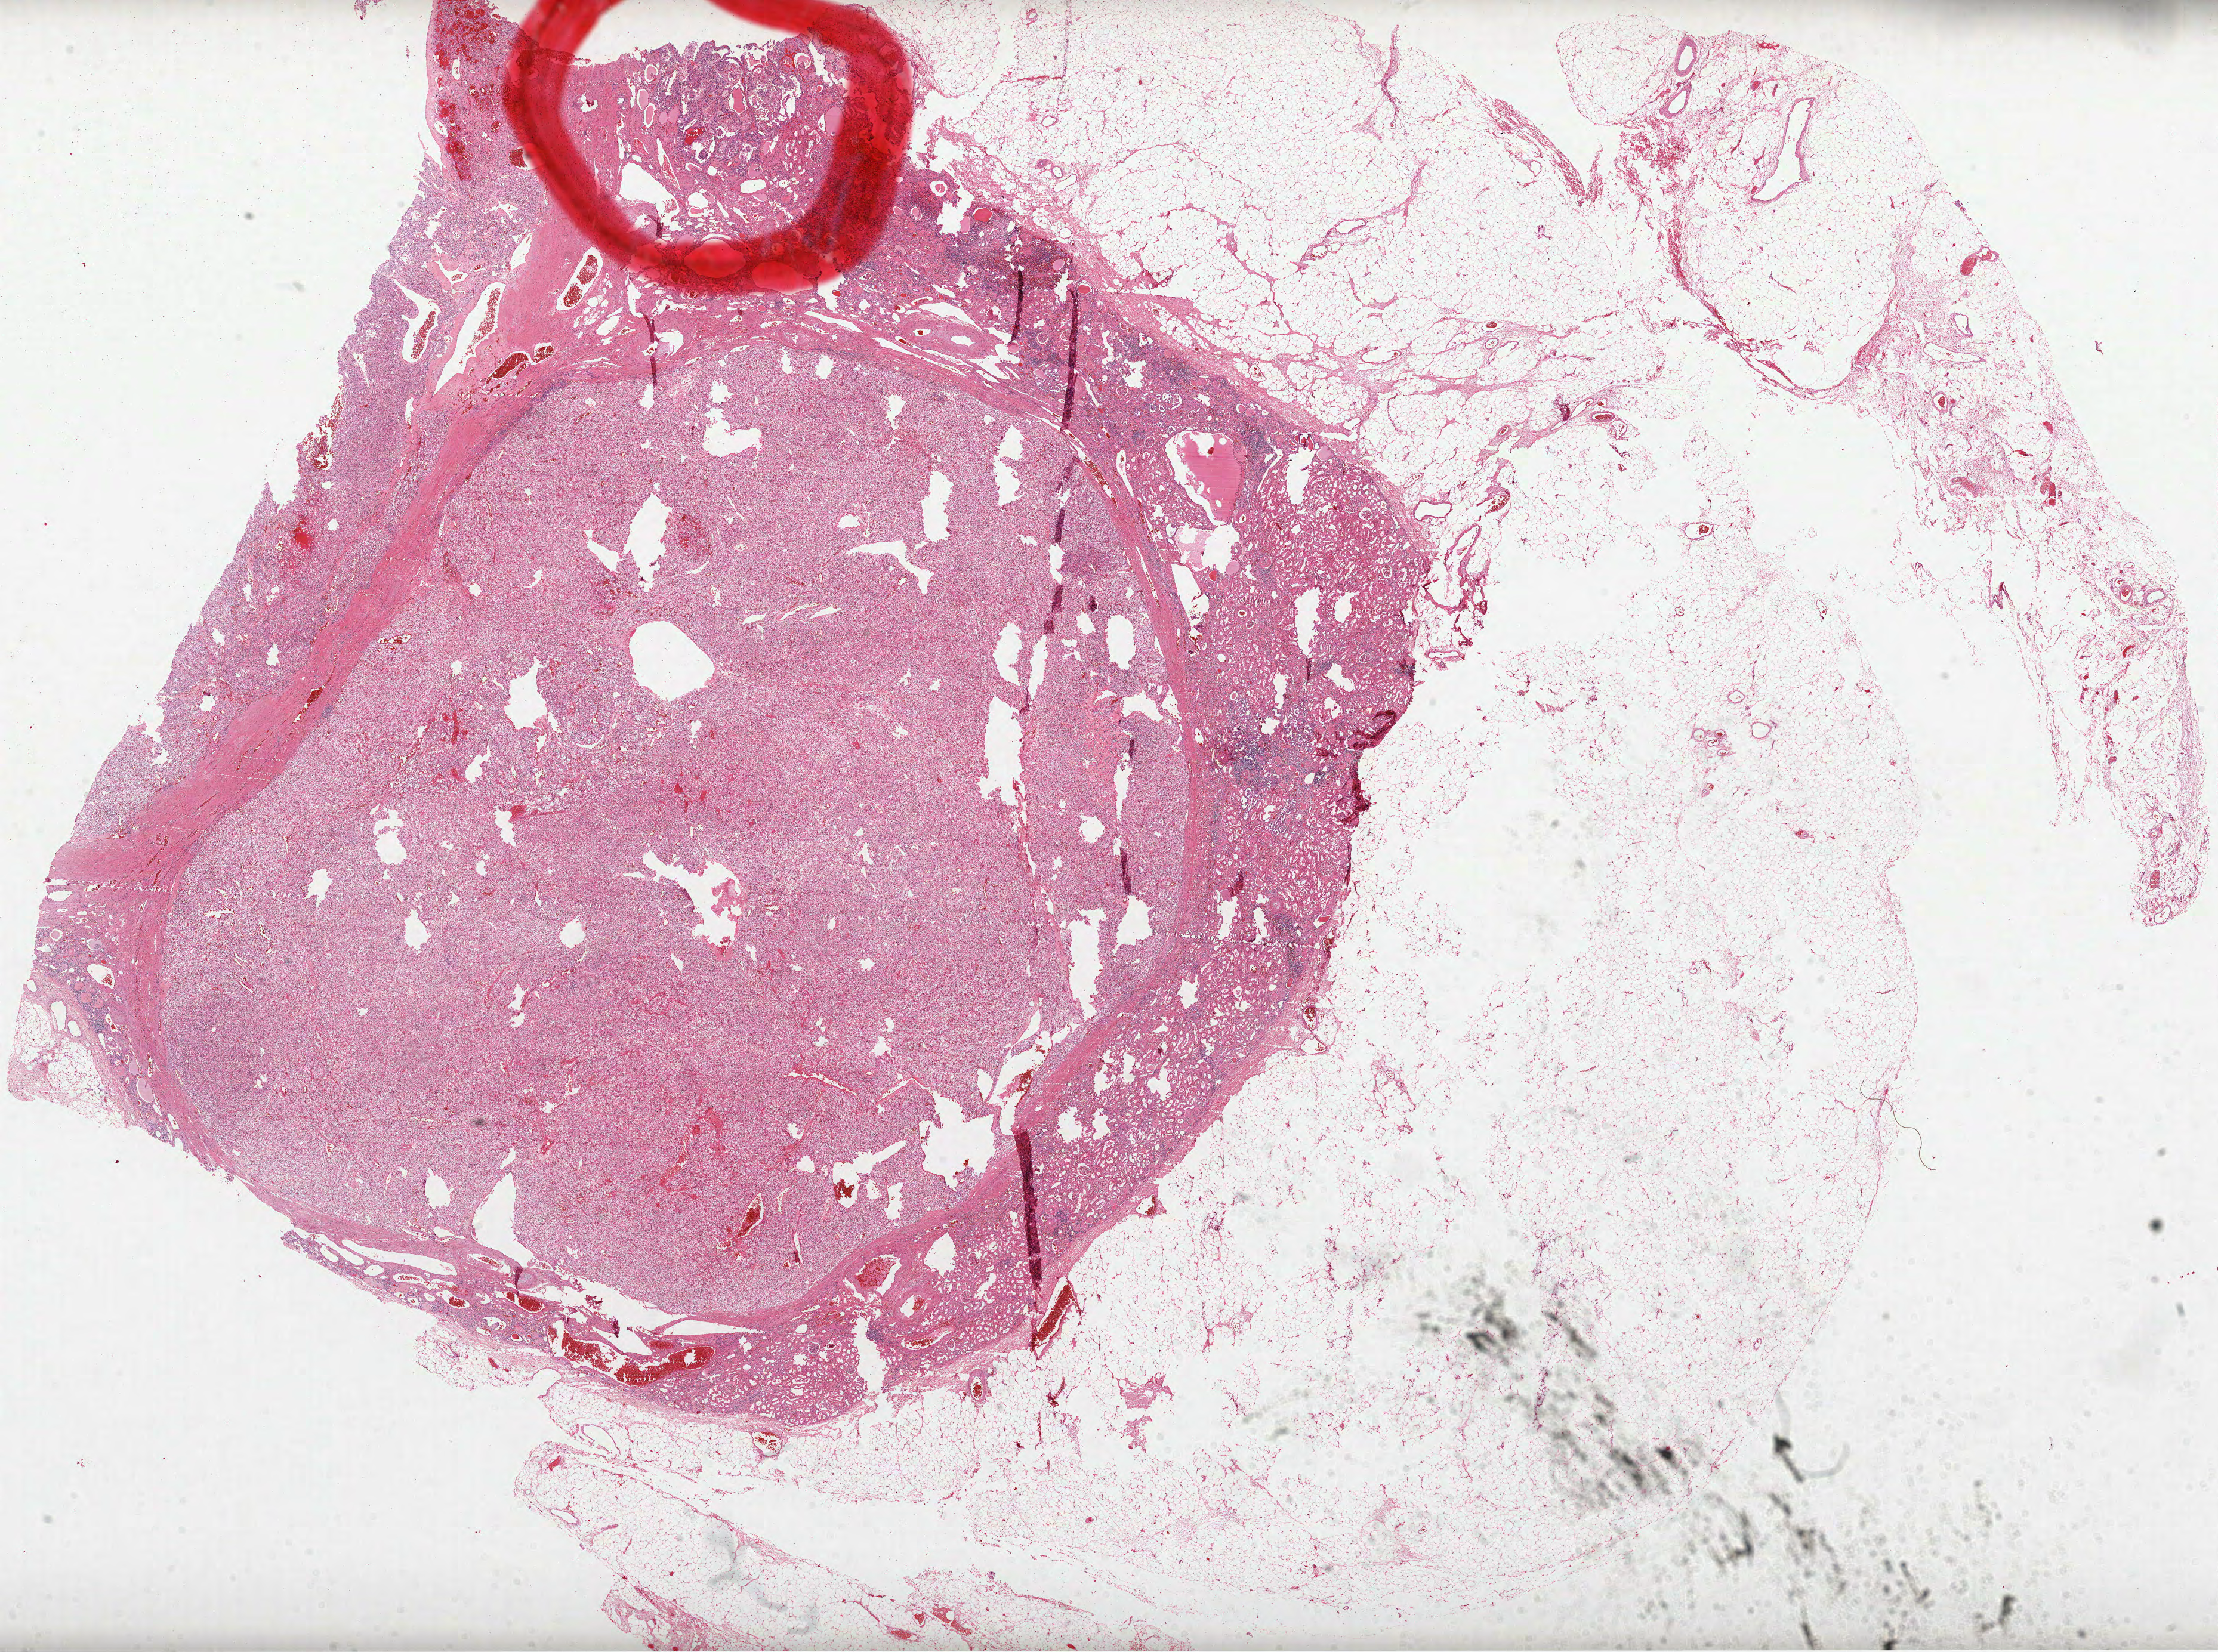
Whole-slide histology image, H&E-stained, shown as a low-resolution overview of the whole scanned area (about 30.0 x 22.3 mm), formalin-fixed paraffin-embedded (FFPE) diagnostic section, sample: primary tumour, kidney. Female patient; age at initial diagnosis 75 years. Histologic grade: G2 (moderately differentiated).
- AJCC pathologic stage: I
- histologic diagnosis: Clear cell adenocarcinoma, NOS